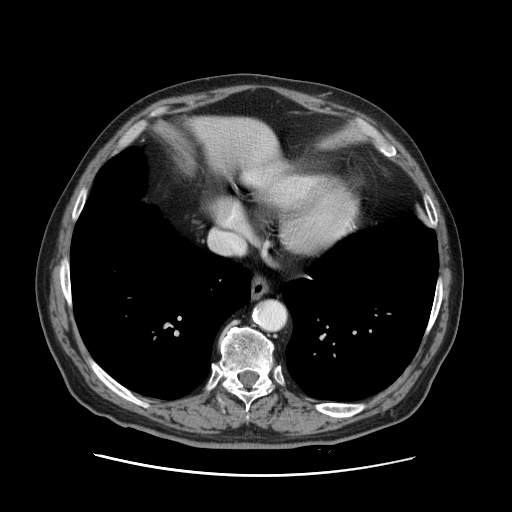
Contrast-enhanced abdominal CT, one axial slice; position 122 of 141 along the scan axis; soft-tissue window (W 400 / L 40 HU); 2.5 mm slice thickness; 512 × 512 image matrix, field of view 395 × 395 mm. Male patient, age 72 years. Case-level facts recorded for this patient, not image findings: diagnosis: colorectal cancer liver metastases, imaged before liver resection; multiple liver metastases: yes; largest metastasis: 5.4 cm.
Outlined on this slice (manually delineated by an expert):
- liver: bounding box (x1, y1, x2, y2) in pixels: (193, 117, 279, 175)
- planned liver remnant (the part of the liver to remain after resection): (193, 117, 279, 176)